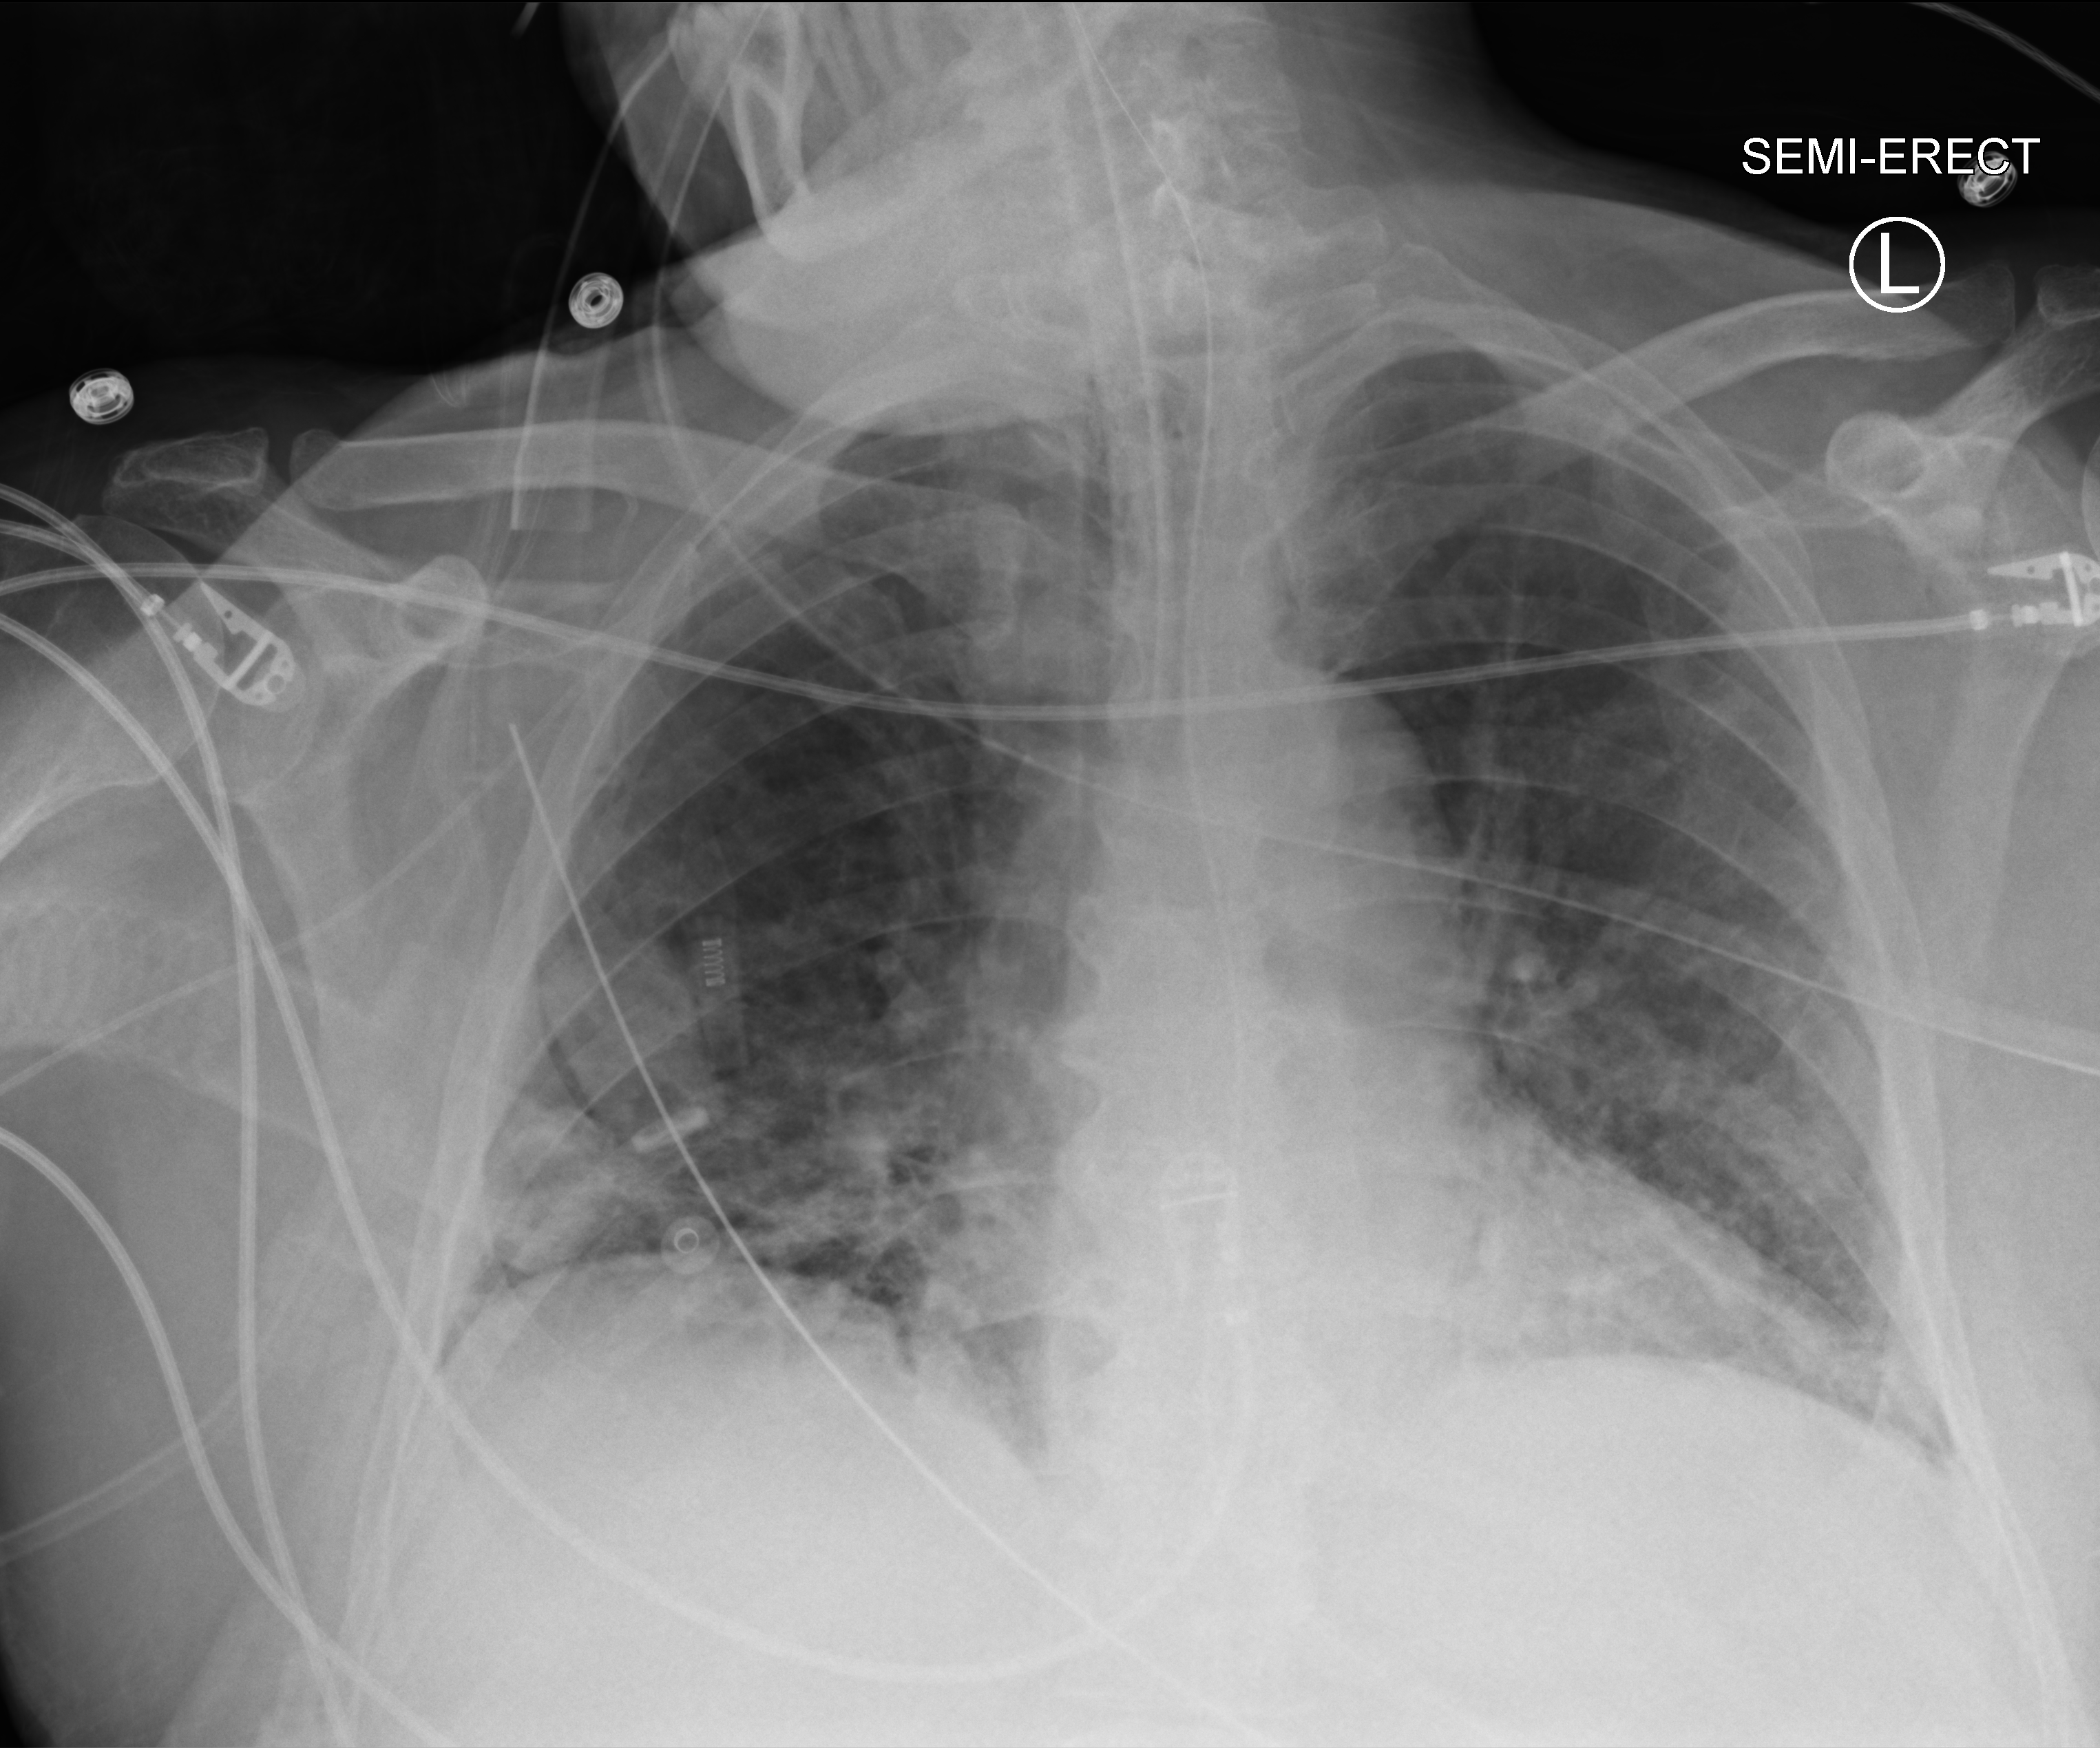
Chest X-ray (portable). Male patient hospitalised with COVID-19, age 60–74 years.
From the hospital-stay record, not from the radiograph (when in the stay this image was taken is not recorded): admitted to intensive care during this hospital stay: yes; length of hospital stay: 26 days; hypertension (admission record): yes.